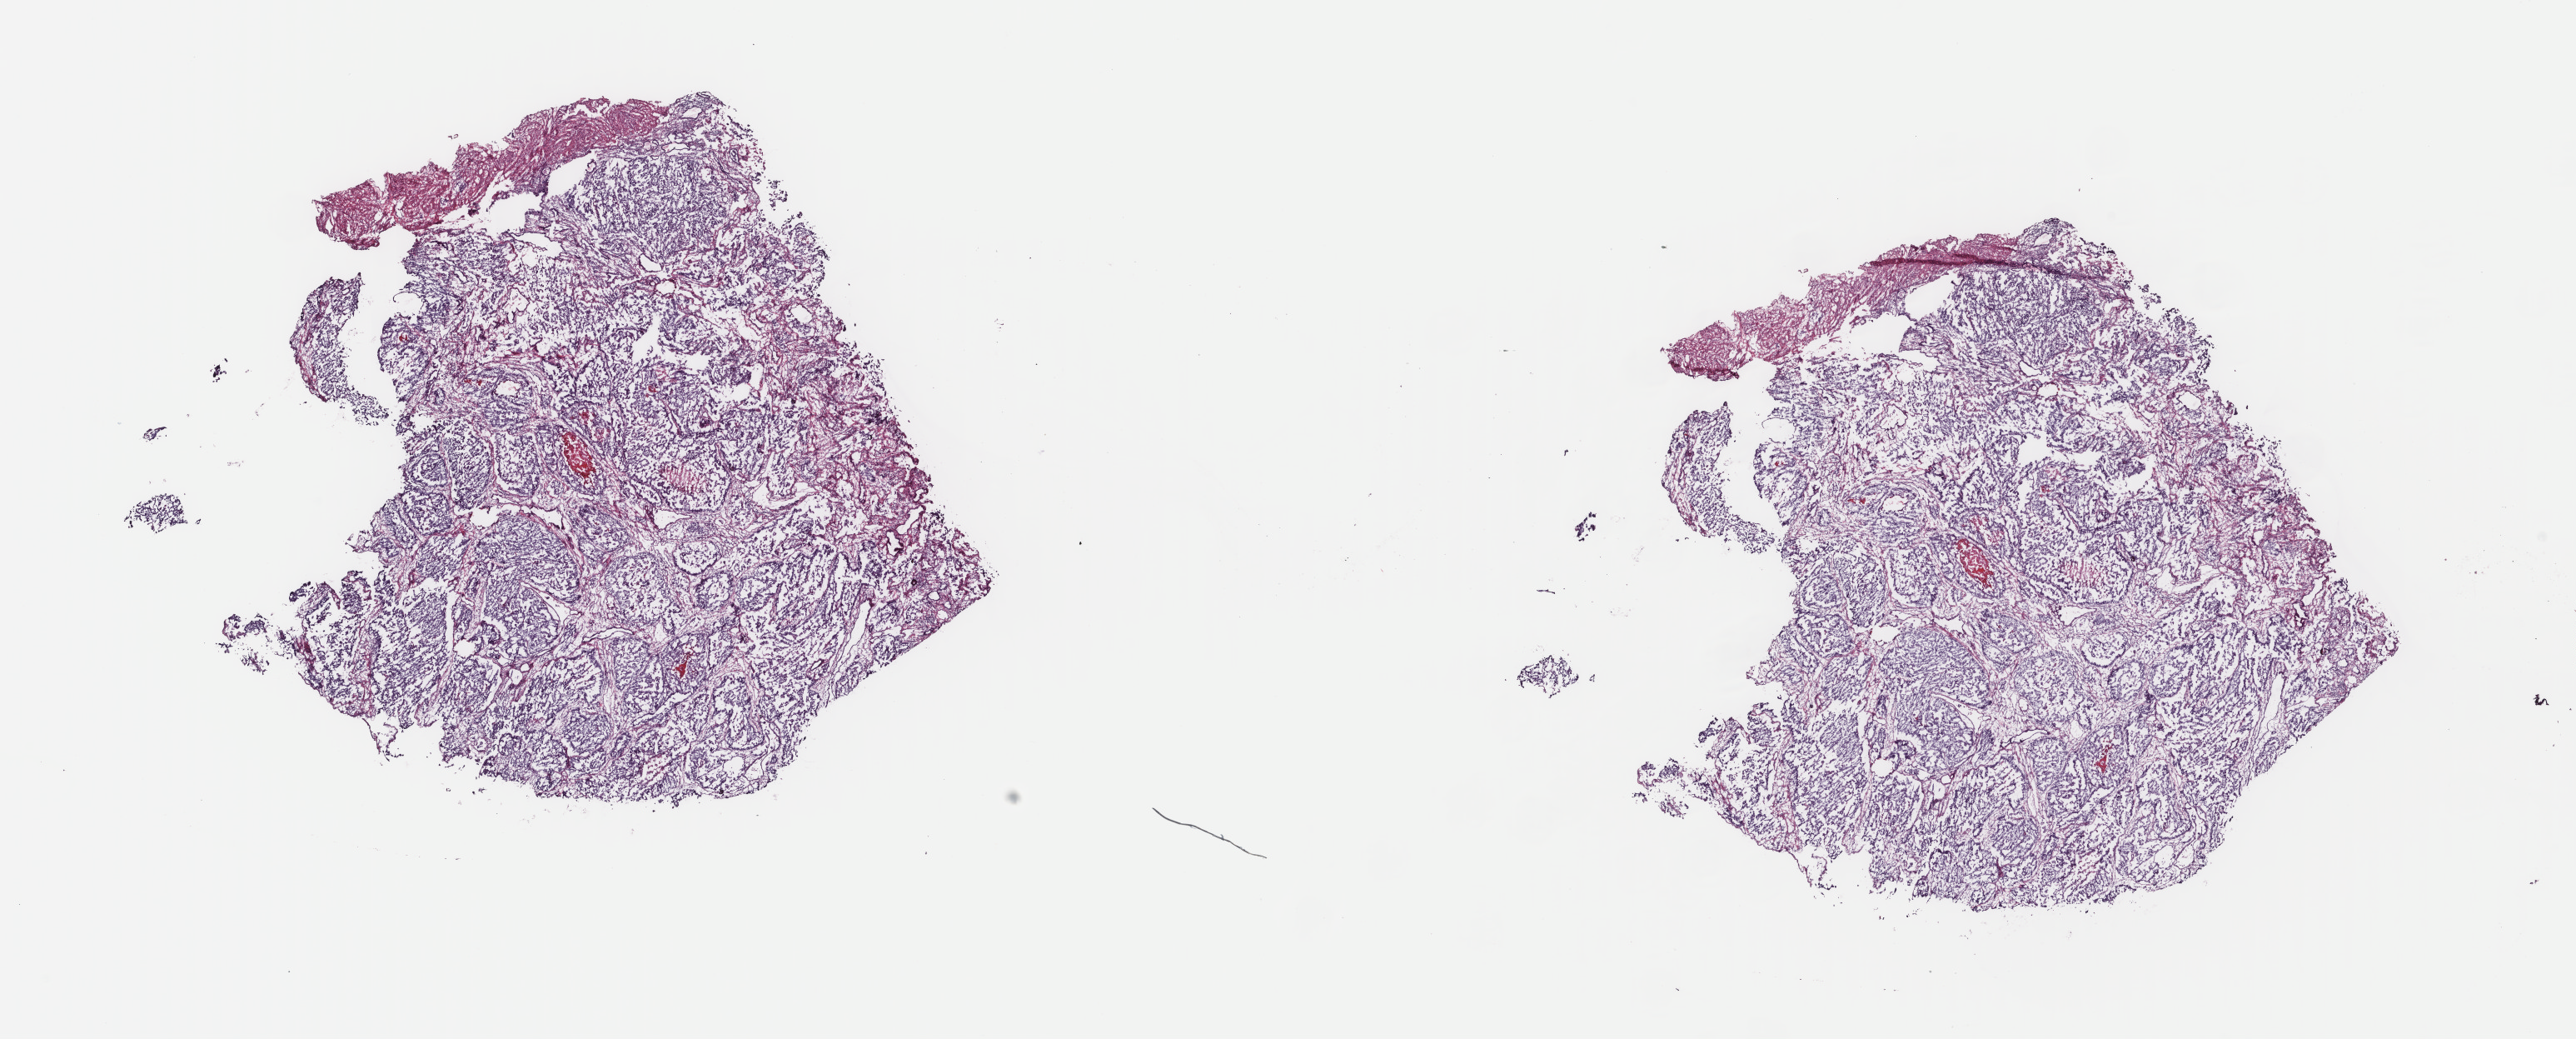
Hematoxylin and eosin (H&E) stained whole-slide image, low-resolution overview of the scanned area, about 24.6 x 9.9 mm (acquisition: 40x scan), frozen section, sample: primary tumour, uterus. Patient: female, age at initial diagnosis 65 years. Histologic grade: G3 (poorly differentiated). Slide review estimates, as recorded: tumour cells 90%, tumour nuclei 90%, normal cells 5%, stromal cells 3%, necrosis 2%. Inflammatory infiltration, as recorded: lymphocyte infiltration 2%, monocyte infiltration 1%, neutrophil infiltration 0%.
Diagnosis: Papillary serous cystadenocarcinoma. FIGO stage: IIIC2.